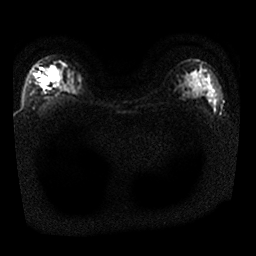
Breast MRI, one axial slice; position 19 of 25 along the scan axis; diffusion-weighted series; image 2 of 4 stored at this slice position (different b-values; order by instance number); 1.5 T; 4 mm slice thickness; 256 × 256 image matrix, field of view 340 × 340 mm. Female patient.
Annotated regions visible in this slice (expert manual segmentation):
- tumour on diffusion-weighted imaging: bounding box (x1, y1, x2, y2) in pixels: (41, 76, 49, 85)